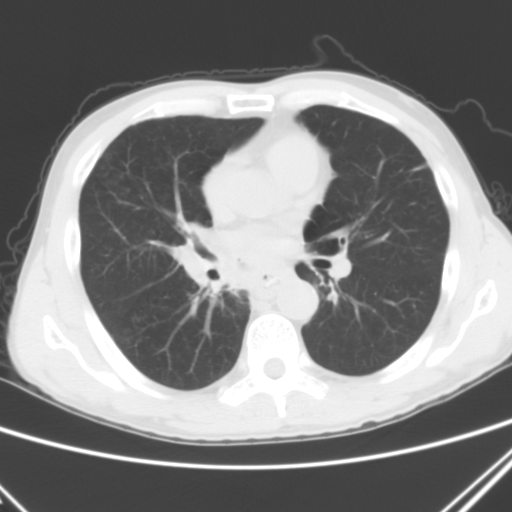
Chest CT, one axial slice. Slice 24 of 51 in the series (ordered by position). 120 kVp. Lung window (W 1500 / L -600 HU). 5 mm slice thickness. 512 × 512 image matrix, field of view 327 × 327 mm. Male patient, age 52 years. Case-level facts recorded for this patient, not image findings: clinical TNM (as recorded): T2a N0 M1c.
Structures marked on this image (rectangle marked by the reading radiologist):
- lung tumour (recorded histology: squamous cell carcinoma): bounding box (x1, y1, x2, y2) in pixels: (173, 221, 236, 307)